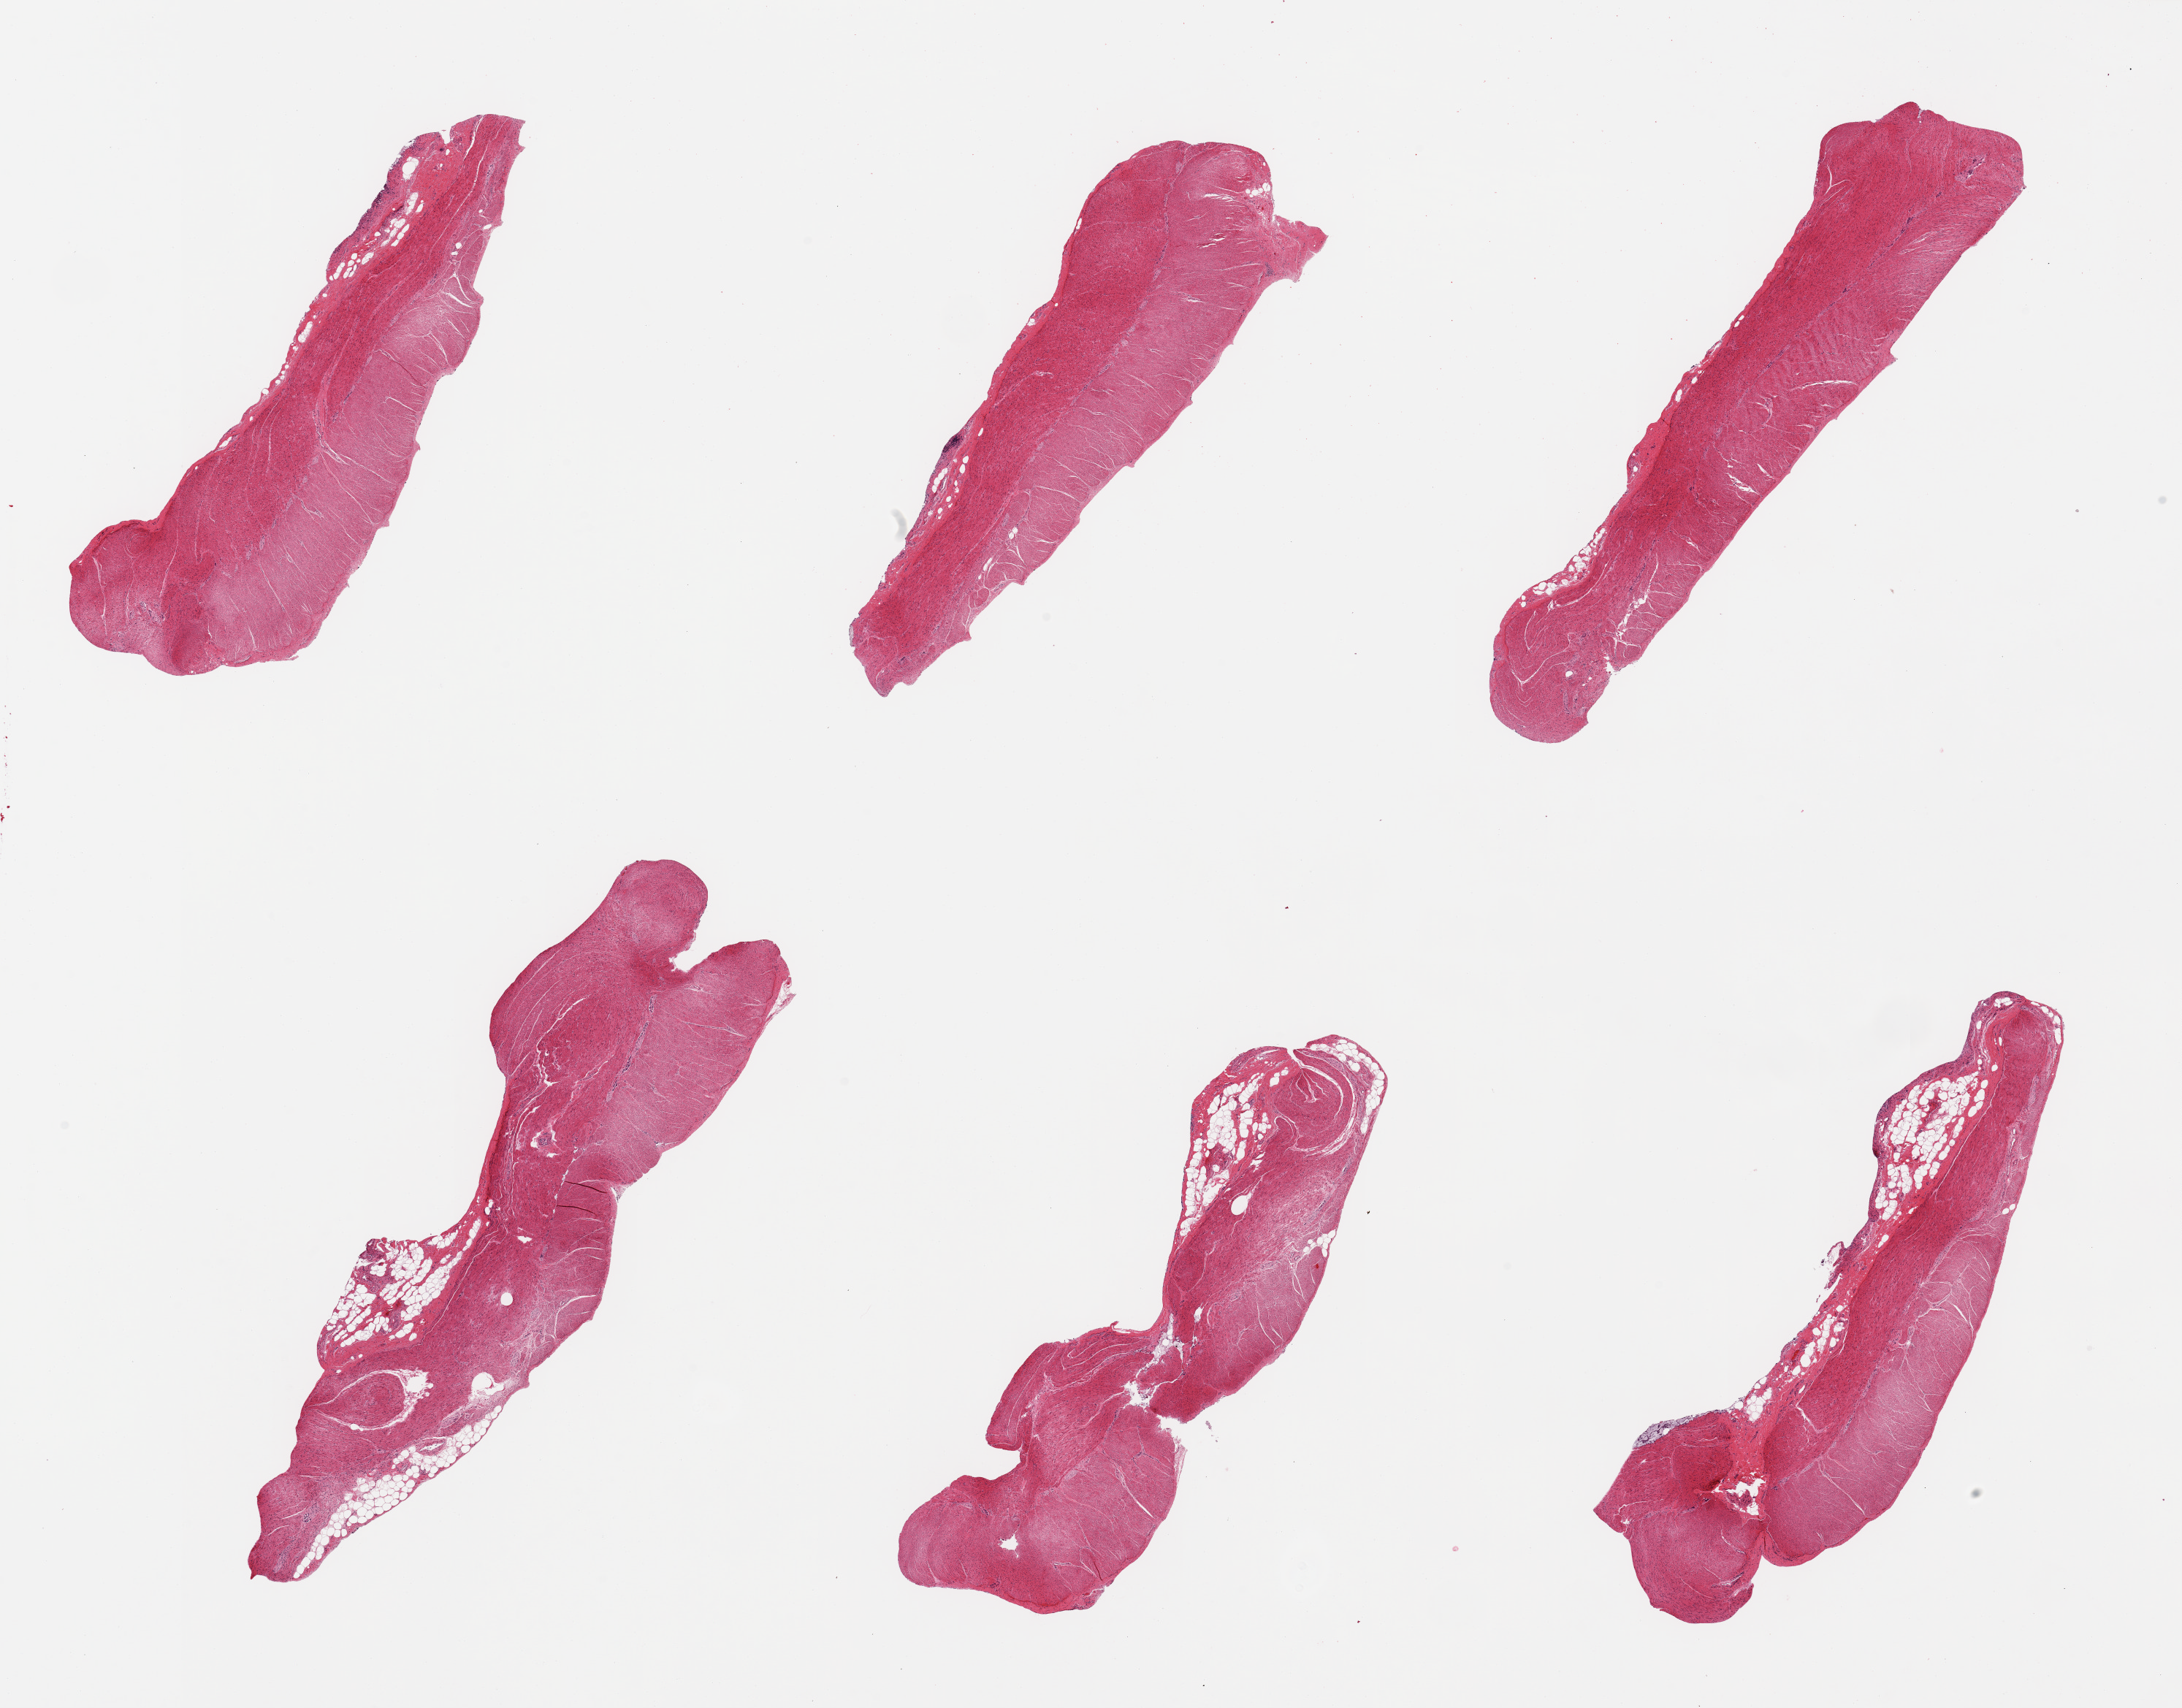
Digitized H&E-stained section, brightfield, a low-resolution overview of the entire scanned area, about 23.6 x 18.5 mm (from a 20x scan). PAXgene-fixed paraffin-embedded (PFPE) section. Section of sigmoid colon (target tissue). Donor tissue sample. Donor: male.
- pathologist's review note for this sample: 6 pieces, confirmed target muscularis